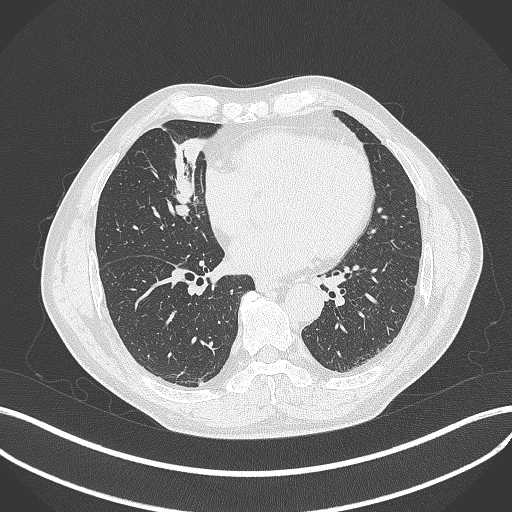
Chest CT, one axial slice; position 162 of 429 along the scan axis; reconstruction kernel B70f; 120 kVp; lung window (W 1500 / L -600 HU); 1 mm slice thickness; 512 × 512 image matrix, field of view 400 × 400 mm. Male patient, age 61 years. Case-level facts recorded for this patient, not image findings: clinical TNM (as recorded): T2b N1 M0.
Structures marked on this image (bounding box drawn by a radiologist):
- lung tumour (recorded histology: squamous cell carcinoma): bounding box [x1, y1, x2, y2] px = [163, 165, 199, 221]